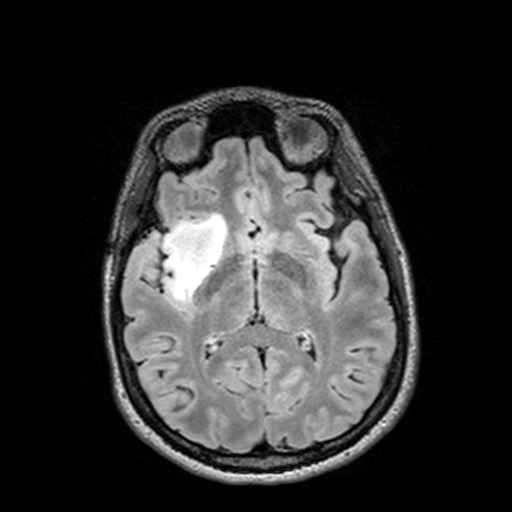
Brain MRI from a brain-tumour surgery series, one axial slice. Position 72 of 144 along the scan axis. T2 FLAIR. 1 mm slice thickness. 512 × 512 image matrix, field of view 250 × 250 mm. From the clinical record (not read from this slice): histopathology: Astrocytoma; WHO grade: 3; IDH mutation: yes; tumour location: Right Insular Temporal.
Outlined on this slice (outlined manually by an expert reader):
- tumour: bounding box (x1, y1, x2, y2) in pixels: (126, 213, 232, 301)